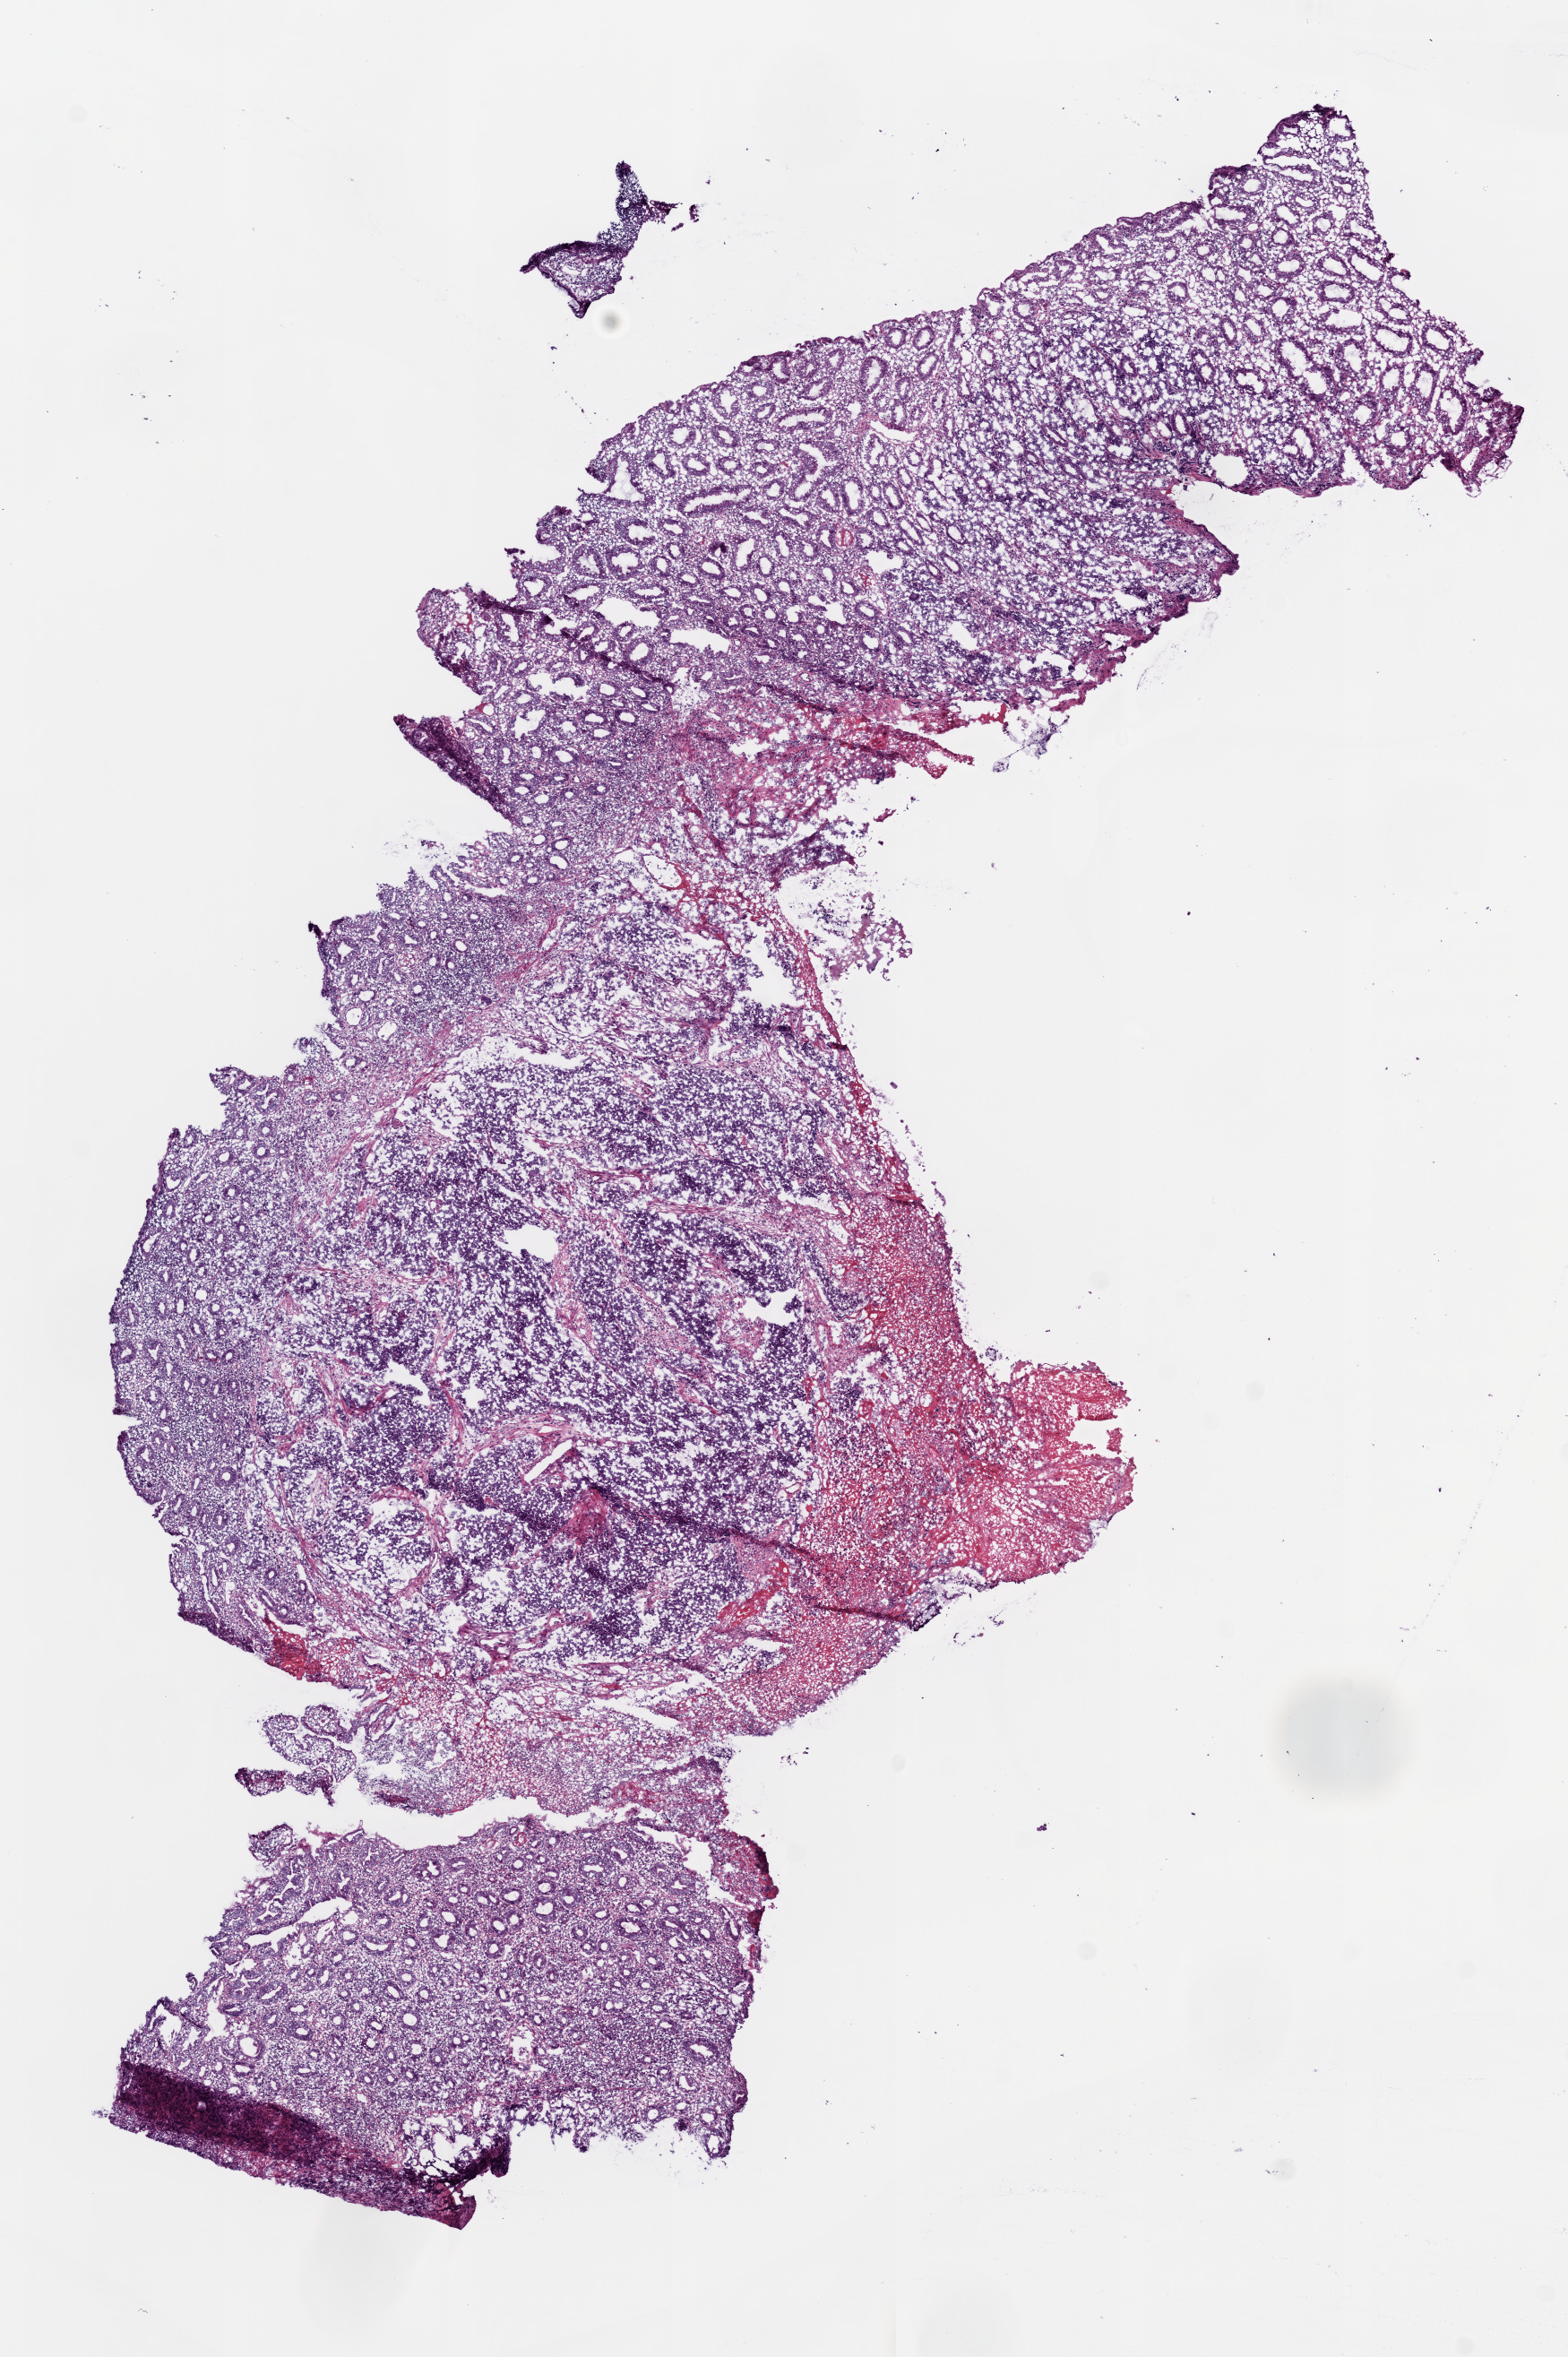
H&E whole-slide image, shown as a low-resolution overview of the whole scanned area (about 7.0 x 10.6 mm, slide scanned at 20x); frozen section from the bottom of the tissue portion; colon, primary tumour sample. Patient: male, age at initial diagnosis 37 years. Composition of this section per pathologist review: tumour nuclei 0%, necrosis 0%.
Histologic diagnosis: Adenocarcinoma, NOS (cecum). AJCC pathologic stage: IV.